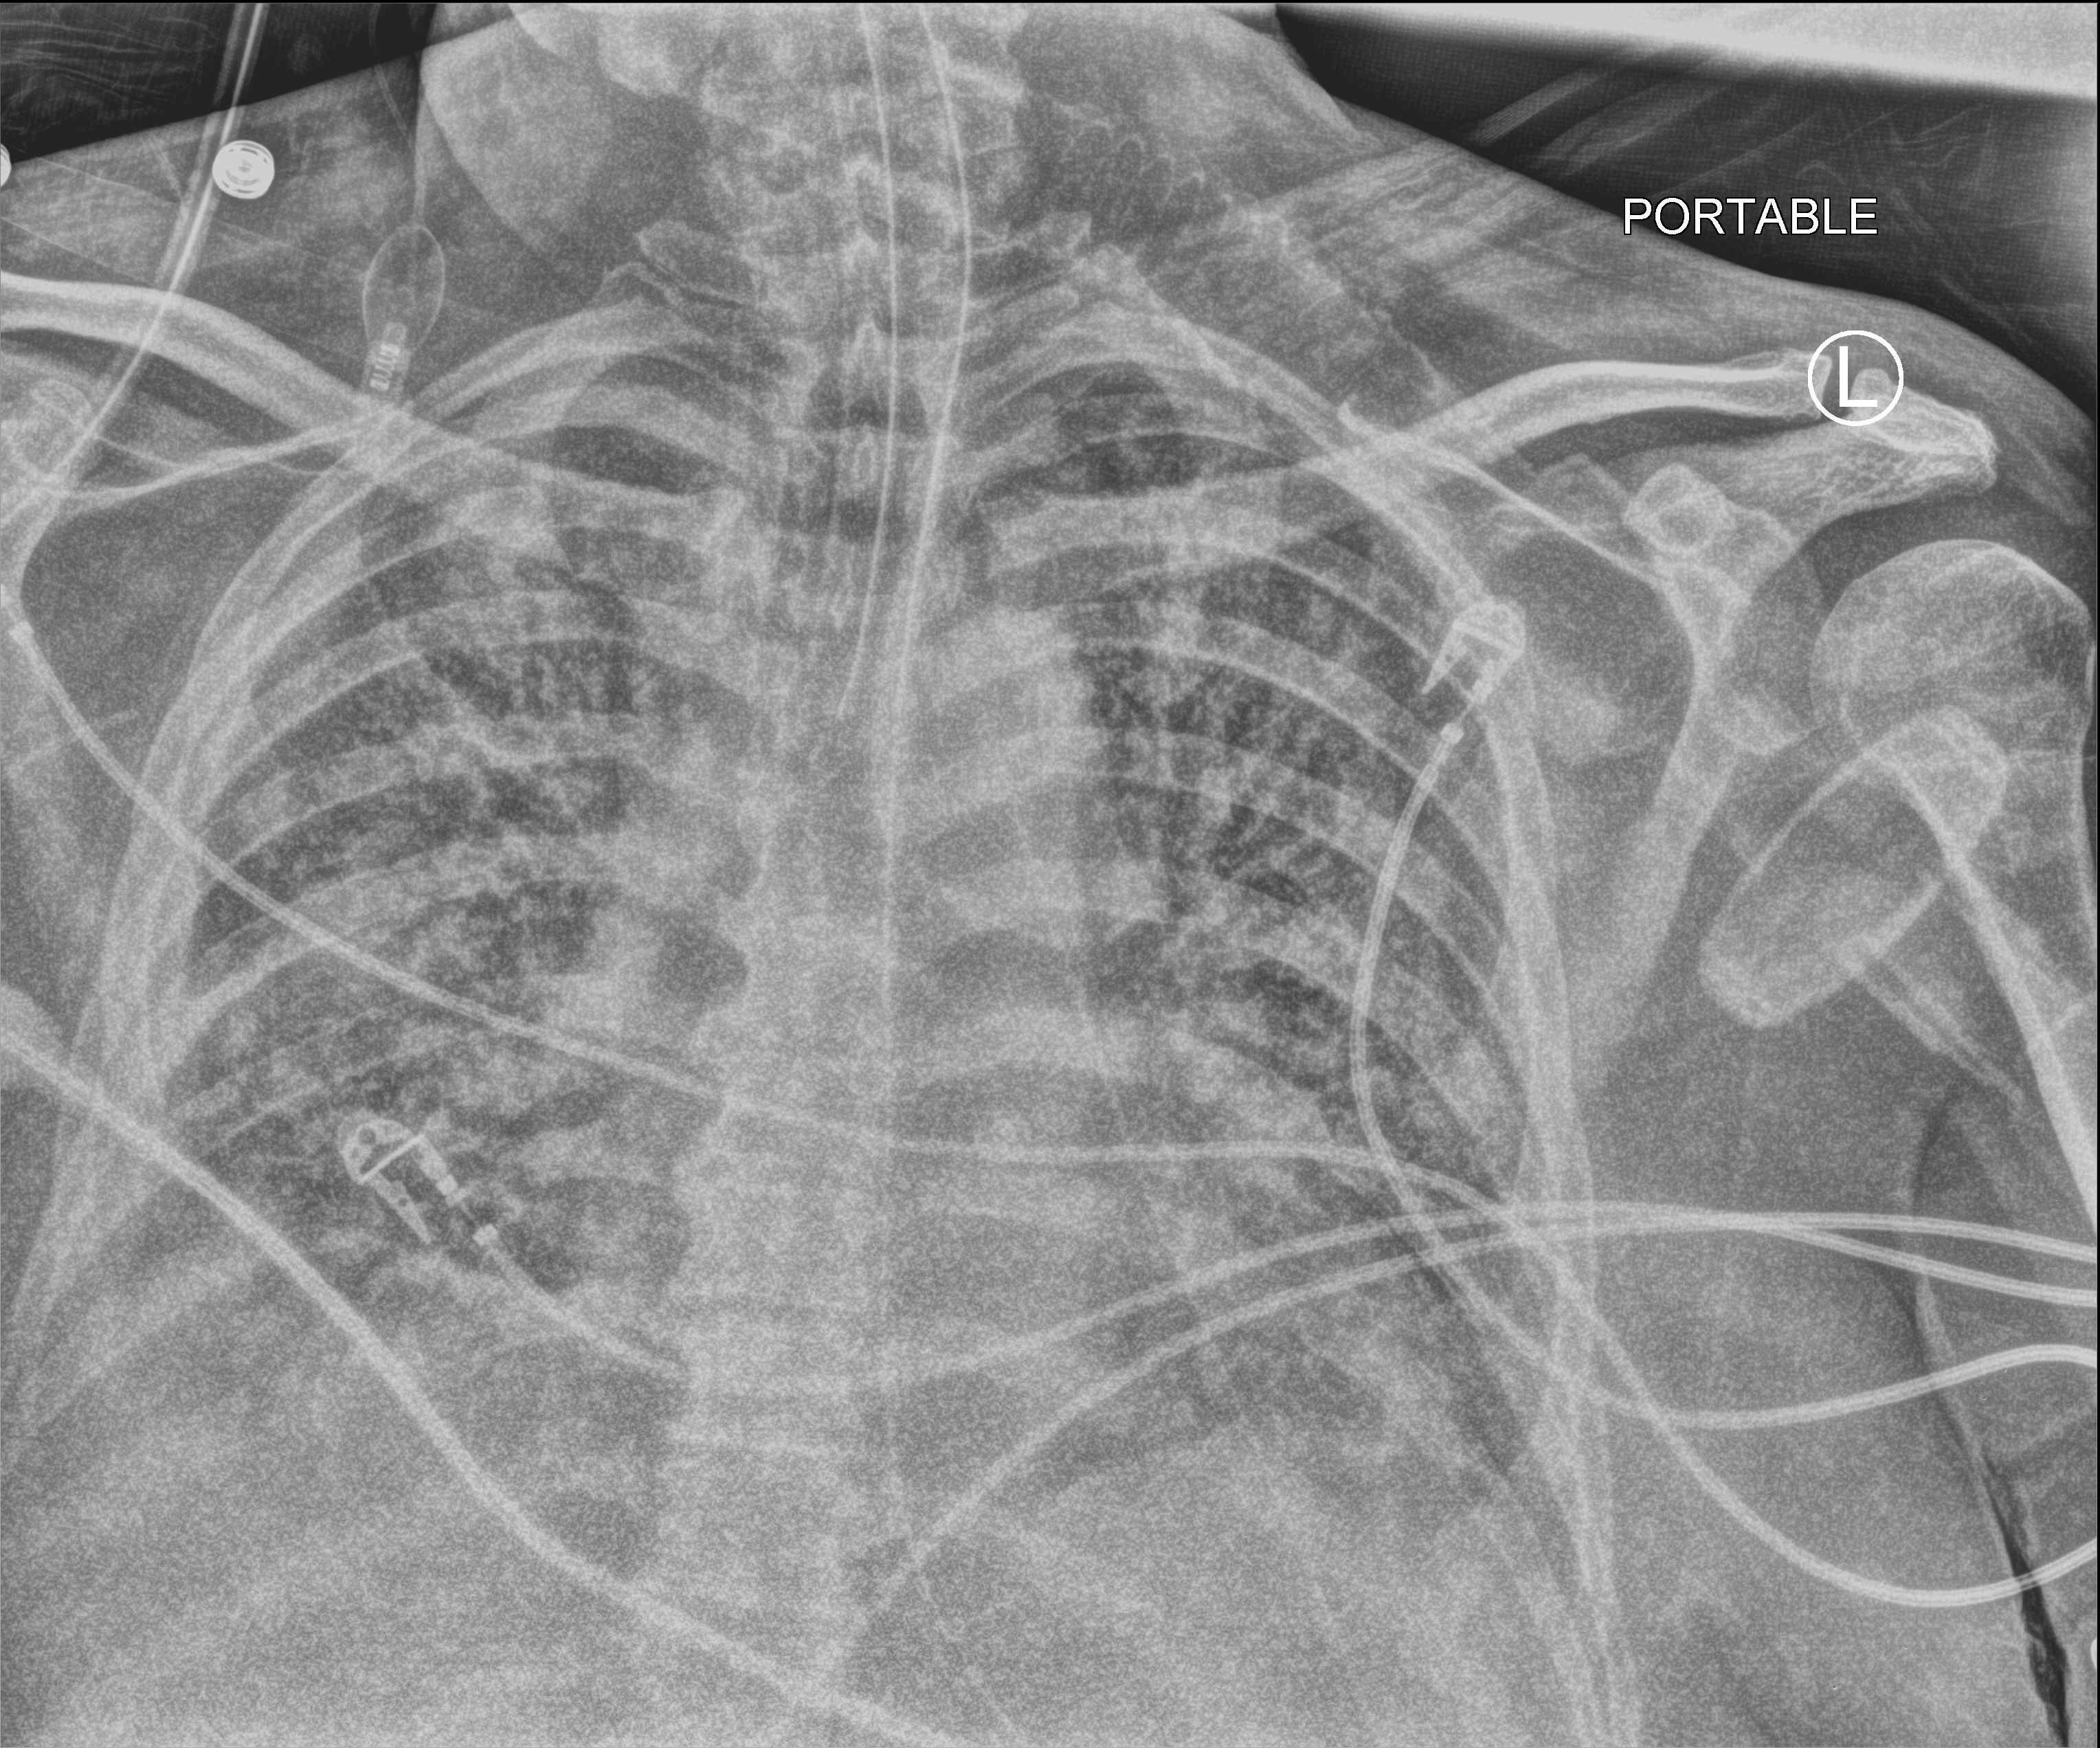
Bedside chest radiograph (computed radiography), anteroposterior (AP) projection. Patient hospitalised with COVID-19; male, aged 60–74 years.
Admission-level facts for this patient (not findings on this image; timing relative to this image not recorded): admitted to intensive care during this hospital stay: yes.